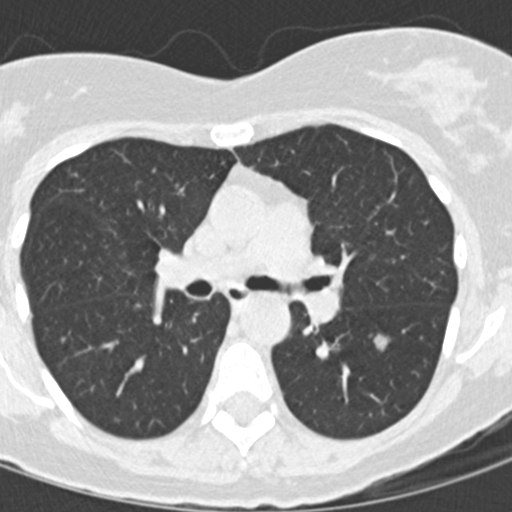
Low-dose screening chest CT, one axial slice. Slice 88 of 145 in the series (ordered by position). 120 kVp. Lung window (W 1500 / L -600 HU). 2 mm slice thickness. 512 × 512 image matrix, field of view 270 × 270 mm.
Structures marked on this image (manually delineated by an expert):
- lesion 1 (tumor, lower lobe of left lung): box from (x=375, y=335) to (x=388, y=350) px